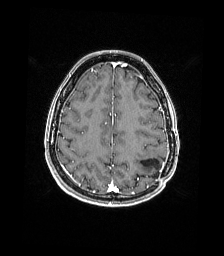
Brain MRI from a brain-tumour surgery series, one axial slice; position 53 of 176 along the scan axis; T1-weighted post-contrast; 1 mm slice thickness; 224 × 256 image matrix, field of view 224 × 256 mm. From the clinical record (not read from this slice): histopathology: Atypical meningioma; WHO grade: 2.
Annotated regions visible in this slice (outlined manually by an expert reader):
- previous resection cavity: bounding box <141,159,161,170> (left, top, right, bottom; pixels)